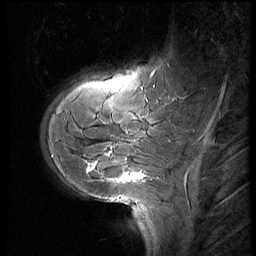
Breast MRI (dynamic contrast-enhanced), one sagittal slice. Slice 15 of 60 in the series (ordered by position). 3 images stored at this slice position (order not interpretable as contrast timing). 1.5 T. TE 4.2 ms, TR 8.9 ms. 256 × 256 image matrix, field of view 200 × 200 mm. Patient: female, 29 years. From the clinical record (not read from this slice): setting: breast cancer imaged before/during neoadjuvant chemotherapy.
Annotated regions visible in this slice (semi-automatic segmentation, software-assisted and operator-edited):
- analysis volume of interest (the breast-tissue region the enhancement analysis was run in; not a lesion): bounding box [x1, y1, x2, y2] px = [42, 57, 185, 200]
- tumour enhancement mask (voxels above the 140 % enhancement threshold inside the analysis volume of interest): [89, 152, 144, 183]